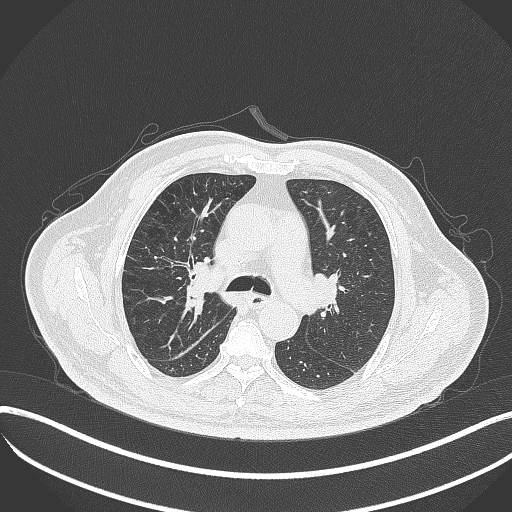
Chest CT, one axial slice. Slice 237 of 401 in the series (ordered by position). Reconstruction kernel B70f. 120 kVp. Lung window (W 1500 / L -600 HU). 512 × 512 image matrix, field of view 400 × 400 mm. Patient: male, 72 years. Case-level facts recorded for this patient, not image findings: clinical TNM (as recorded): T1c N0 M0.
Annotated regions visible in this slice (bounding box drawn by a radiologist):
- lung tumour (recorded histology: squamous cell carcinoma): bounding box [x1, y1, x2, y2] px = [180, 262, 212, 311]